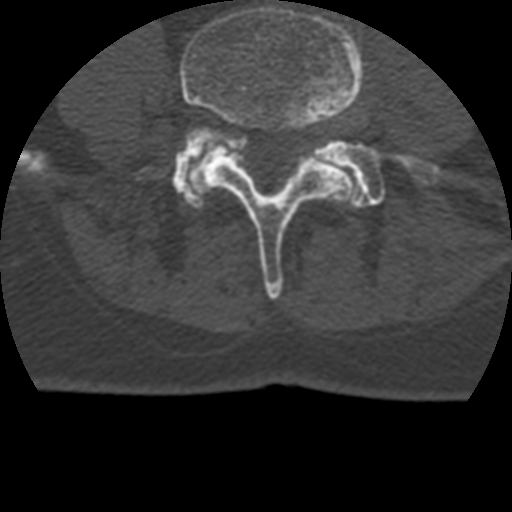
CT including the spine, one axial slice; slice 59 of 399 in the series (ordered by position); reconstruction kernel STANDARD; 120 kVp; bone window (W 1800 / L 400 HU); 1.25 mm slice thickness; 512 × 512 image matrix. Patient age 69 years. Case-level facts recorded for this patient, not image findings: primary cancer: prostate.
Structures marked on this image (semi-automatic segmentation, software-assisted and operator-edited):
- L4 vertebra: bounding box [x1, y1, x2, y2] px = [180, 6, 365, 299]
- L5 vertebra: [172, 133, 432, 207]